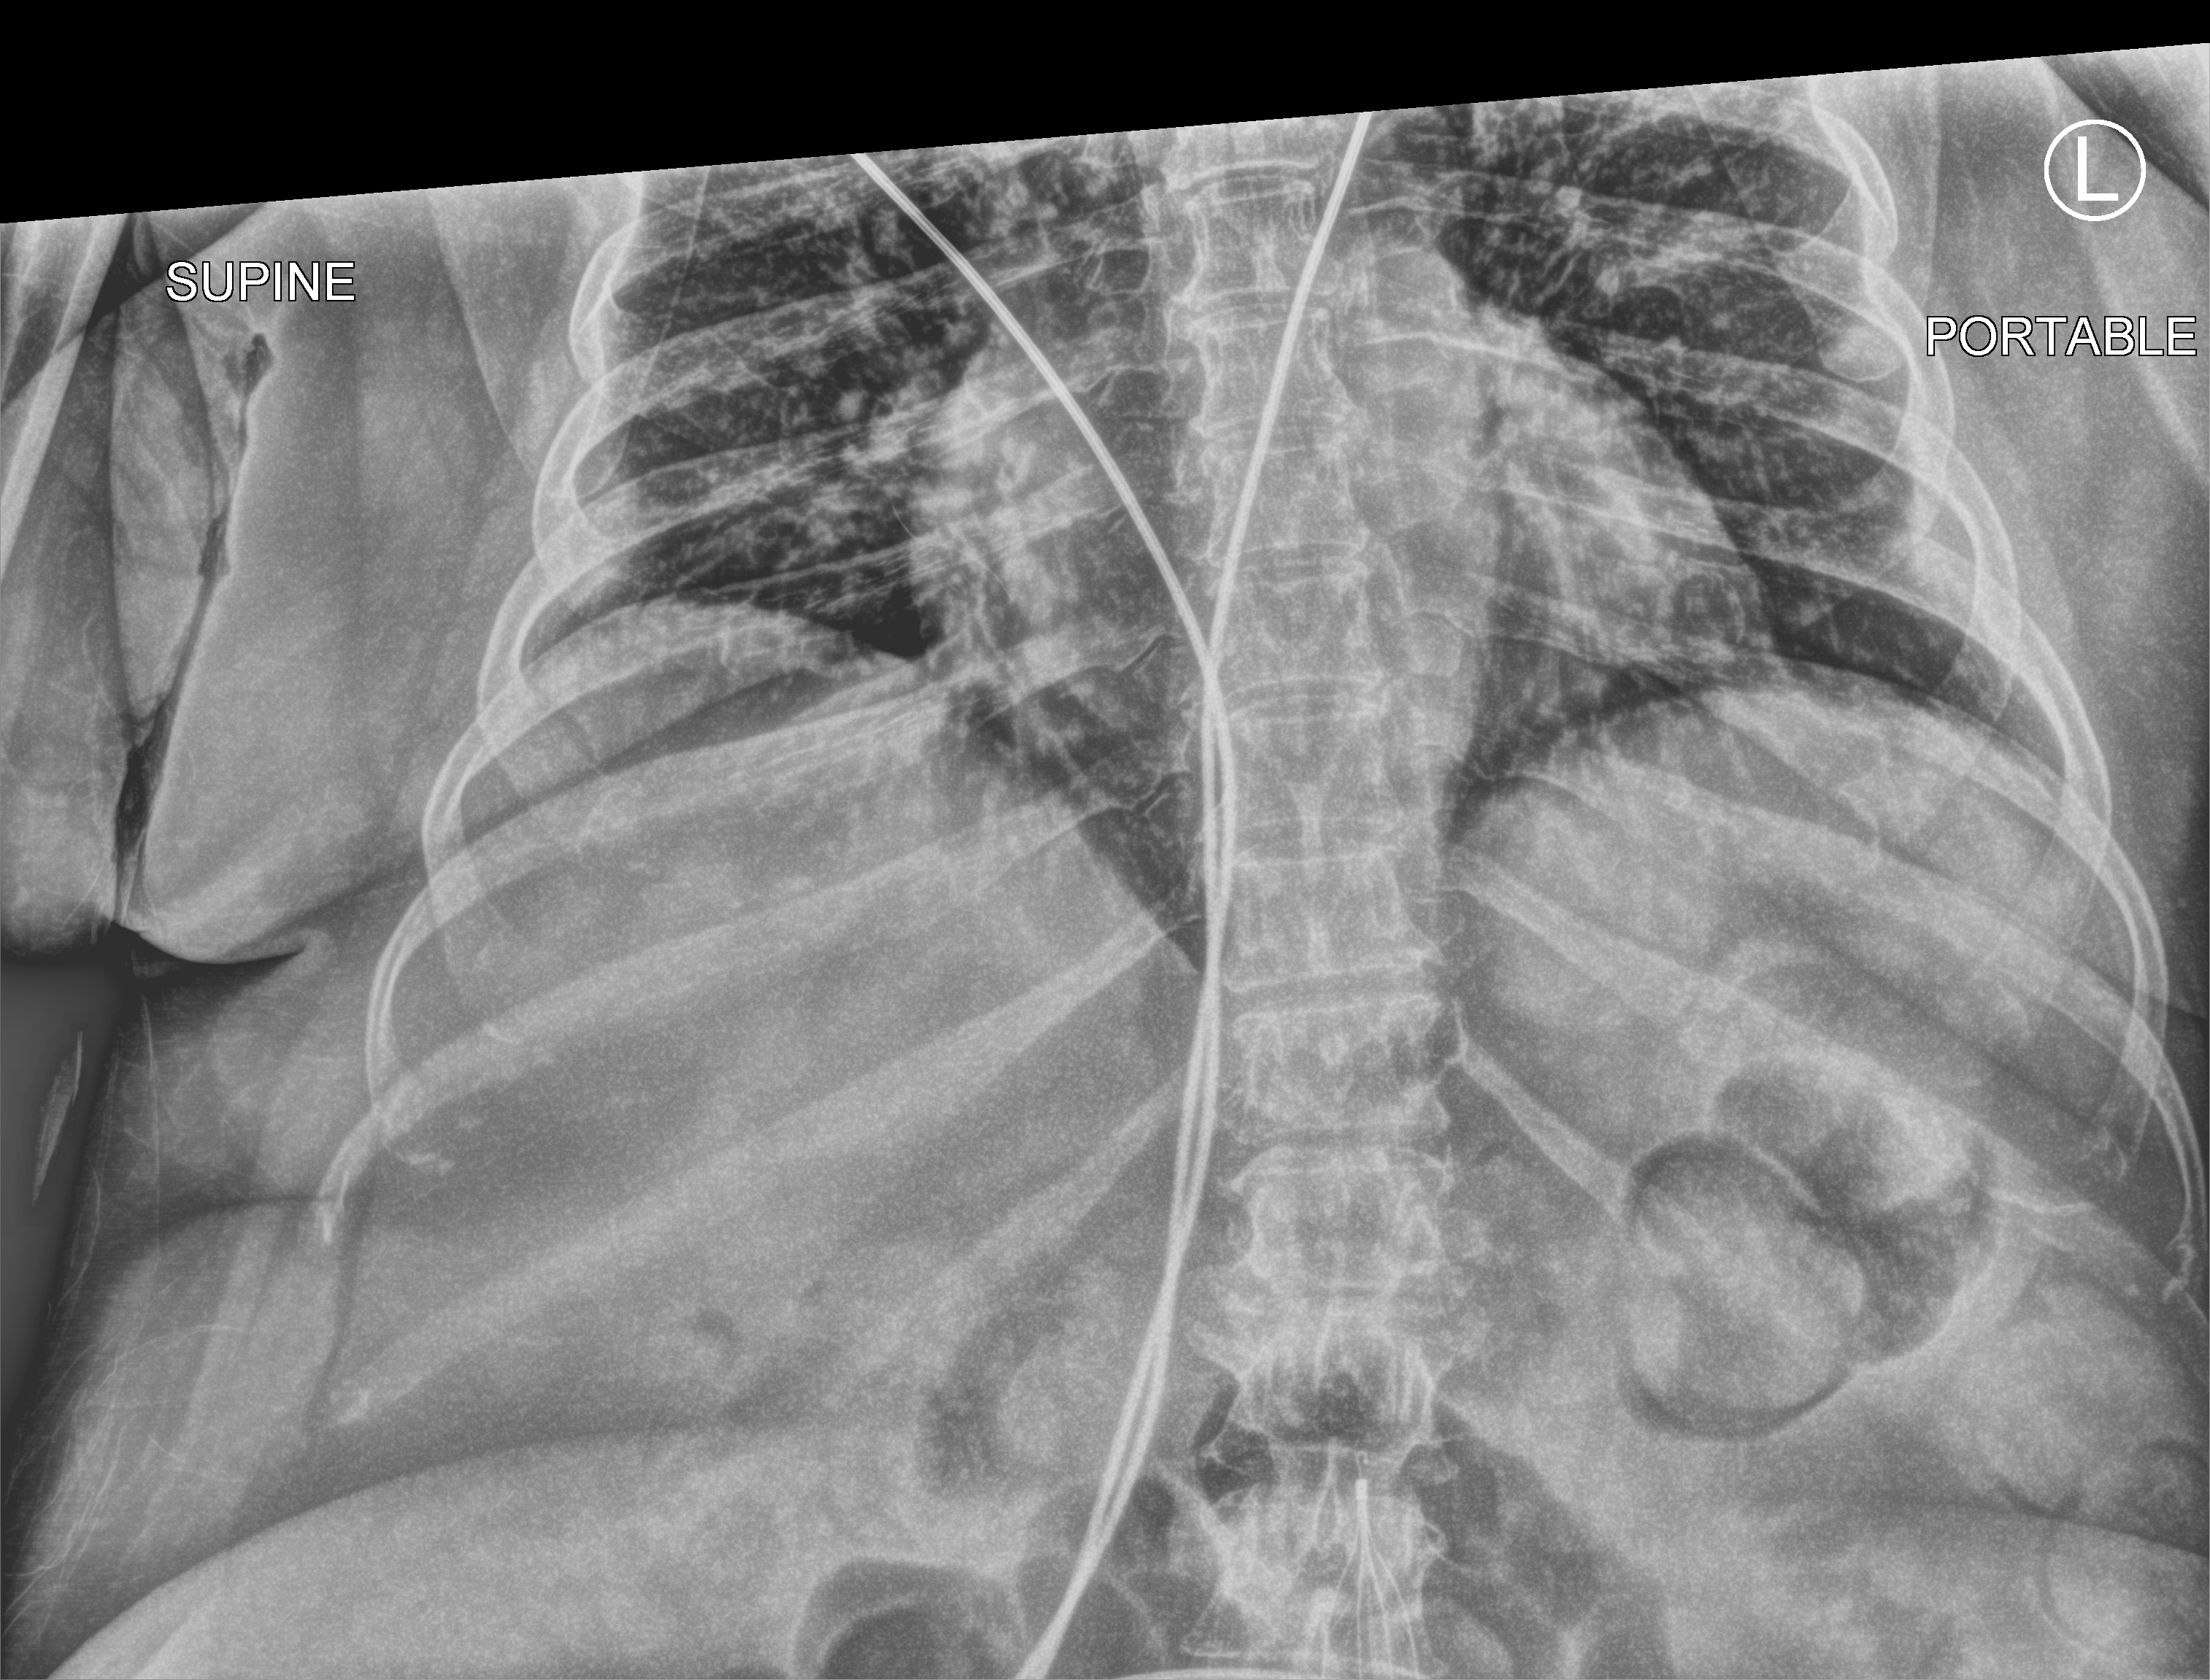
Abdomen X-ray (portable); anteroposterior (AP) projection. Female patient hospitalised with COVID-19, age 60–74 years.
Hospital-stay facts (about this admission, not read from this image; timing relative to this image not recorded):
- mechanically ventilated during this hospital stay: no
- admitted to intensive care during this hospital stay: no